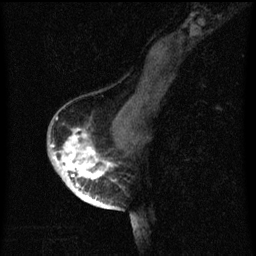
Breast MRI (dynamic contrast-enhanced), one sagittal slice. Slice 38 of 60 in the series (ordered by position). Dynamic contrast-enhanced series, image 2 of 3 at this slice position (ordered by acquisition). 1.5 T. TE 4.2 ms, TR 8 ms. 2 mm slice thickness. 256 × 256 image matrix. Female patient, age 56 years.
Outlined on this slice (semi-automatically segmented with operator editing):
- analysis volume of interest (the breast-tissue region the enhancement analysis was run in; not a lesion): bounding box (x1, y1, x2, y2) in pixels: (54, 122, 120, 199)
- tumour enhancement mask (voxels above the 70 % enhancement threshold inside the analysis volume of interest): (54, 130, 114, 199)